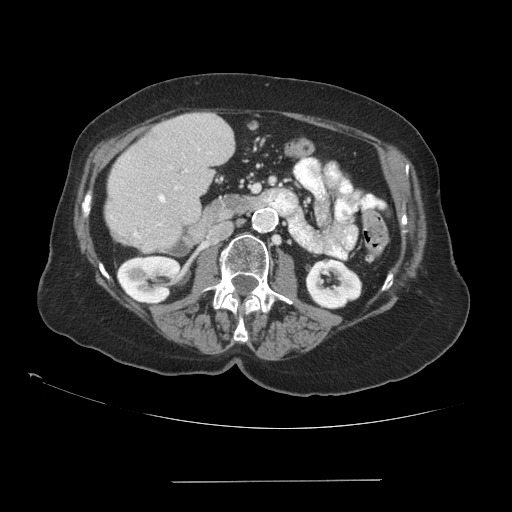
Contrast-enhanced abdominal CT (liver protocol), one axial slice; position 33 of 89 along the scan axis; reconstruction kernel STANDARD; 140 kVp; soft-tissue window (W 400 / L 40 HU); 2.5 mm slice thickness; 512 × 512 image matrix, field of view 400 × 400 mm. From the clinical record (not read from this slice): diagnosis: hepatocellular carcinoma (patient treated with transarterial chemoembolisation; whether this scan precedes or follows treatment is not stated here); TNM stage (as recorded): Stage-IVA; Child-Pugh class: A; tumour nodularity: uninodular.
Outlined on this slice (semi-automatic segmentation, software-assisted and operator-edited):
- liver parenchyma outside the tumour (the mass and vessels are separate outlines, so this box may not span the whole liver): bounding box [x1, y1, x2, y2] px = [104, 112, 234, 252]
- mass: [146, 127, 164, 147]
- liver vessels: [134, 149, 200, 238]